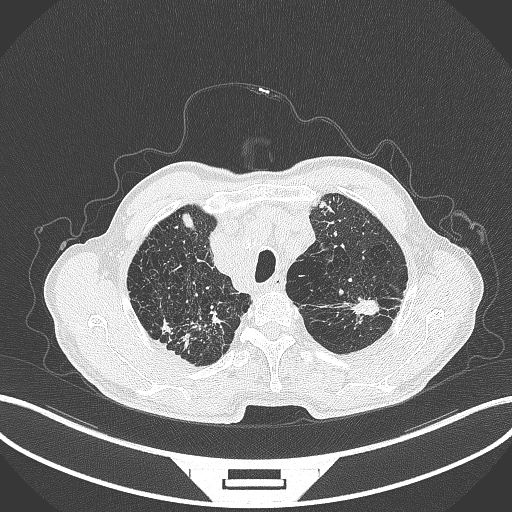
Chest CT, one axial slice. Slice 375 of 463 in the series (ordered by position). Reconstruction kernel B70f. 120 kVp. Lung window (W 1500 / L -600 HU). 512 × 512 image matrix, field of view 400 × 400 mm. Patient: male, 74 years. From the clinical record (not read from this slice): clinical TNM (as recorded): T2a N1 M0.
Annotated regions visible in this slice (bounding box drawn by a radiologist):
- lung tumour (recorded histology: adenocarcinoma): bounding box [x1, y1, x2, y2] px = [350, 293, 383, 318]